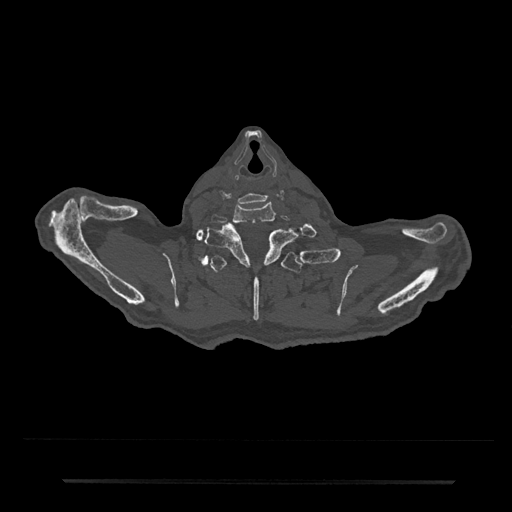
CT including the spine, one axial slice. Position 718 of 797 along the scan axis. Reconstruction kernel Br40s/3. 120 kVp. Bone window (W 1800 / L 400 HU). 512 × 512 image matrix. Male patient, age 74 years. From the clinical record (not read from this slice): primary cancer: prostate.
Structures marked on this image (semi-automatically segmented with operator editing):
- T1 vertebra: bounding box <205,223,298,266> (left, top, right, bottom; pixels)
- T2 vertebra: <201,252,314,321>